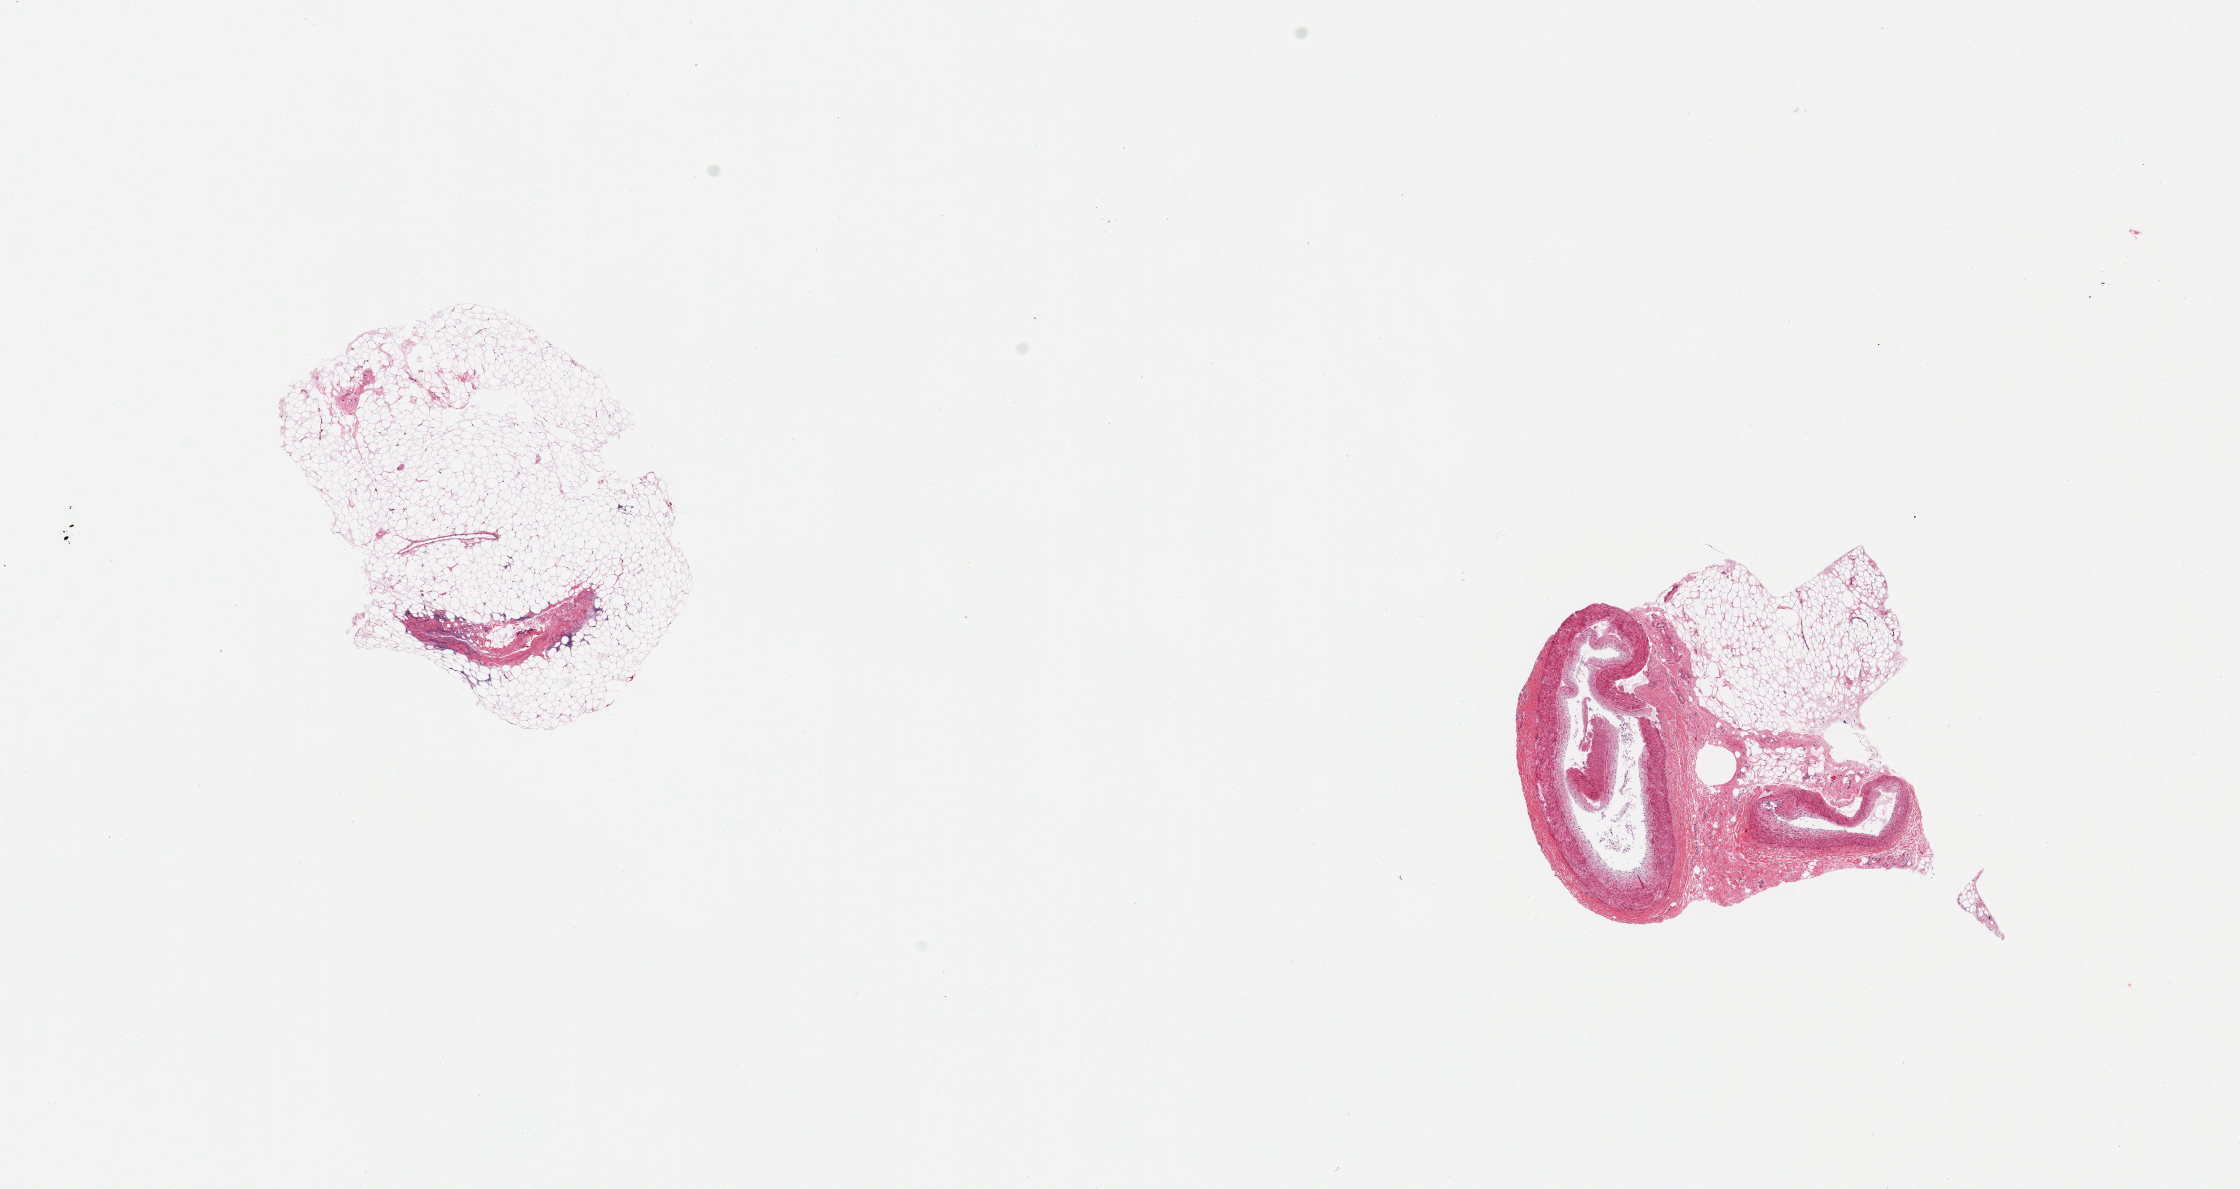
H&E whole-slide image, low-resolution overview of the scanned area, about 17.7 x 9.4 mm, PAXgene-fixed paraffin-embedded (PFPE) section, sampled site (target tissue): coronary artery, donor tissue sample. Donor sex: female.
Pathologist's review note for this sample: 2 pieces; 1 piece has only fibrofatty tissue, no artery; other contains 50% fibrofatty tissue and 2 arteries.